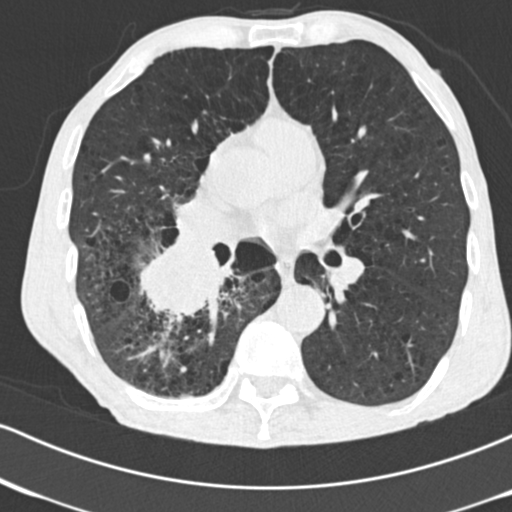
Axial slice from a low-dose chest CT screening exam, second screening round (one year after baseline), lung window (W 1500 / L -600 HU), slice 96 of 182 in the series. Male, age 64 years at enrolment. Current smoker at enrolment.
Expert reader's lesion annotation, bounding box [x1, y1, x2, y2] px = [129, 228, 241, 332]. Reader record for this screening exam (exam-level; its link to the box is not recorded): non-calcified nodule or mass ≥4 mm, 52 × 37 mm, spiculated (stellate) margins, soft tissue attenuation, pre-existing on the prior screen: no. Participant outcome: lung cancer diagnosed 28 days after this screen — adenocarcinoma, NOS, right lower lobe, stage IV (AJCC 6th edition), 60 mm at pathology.